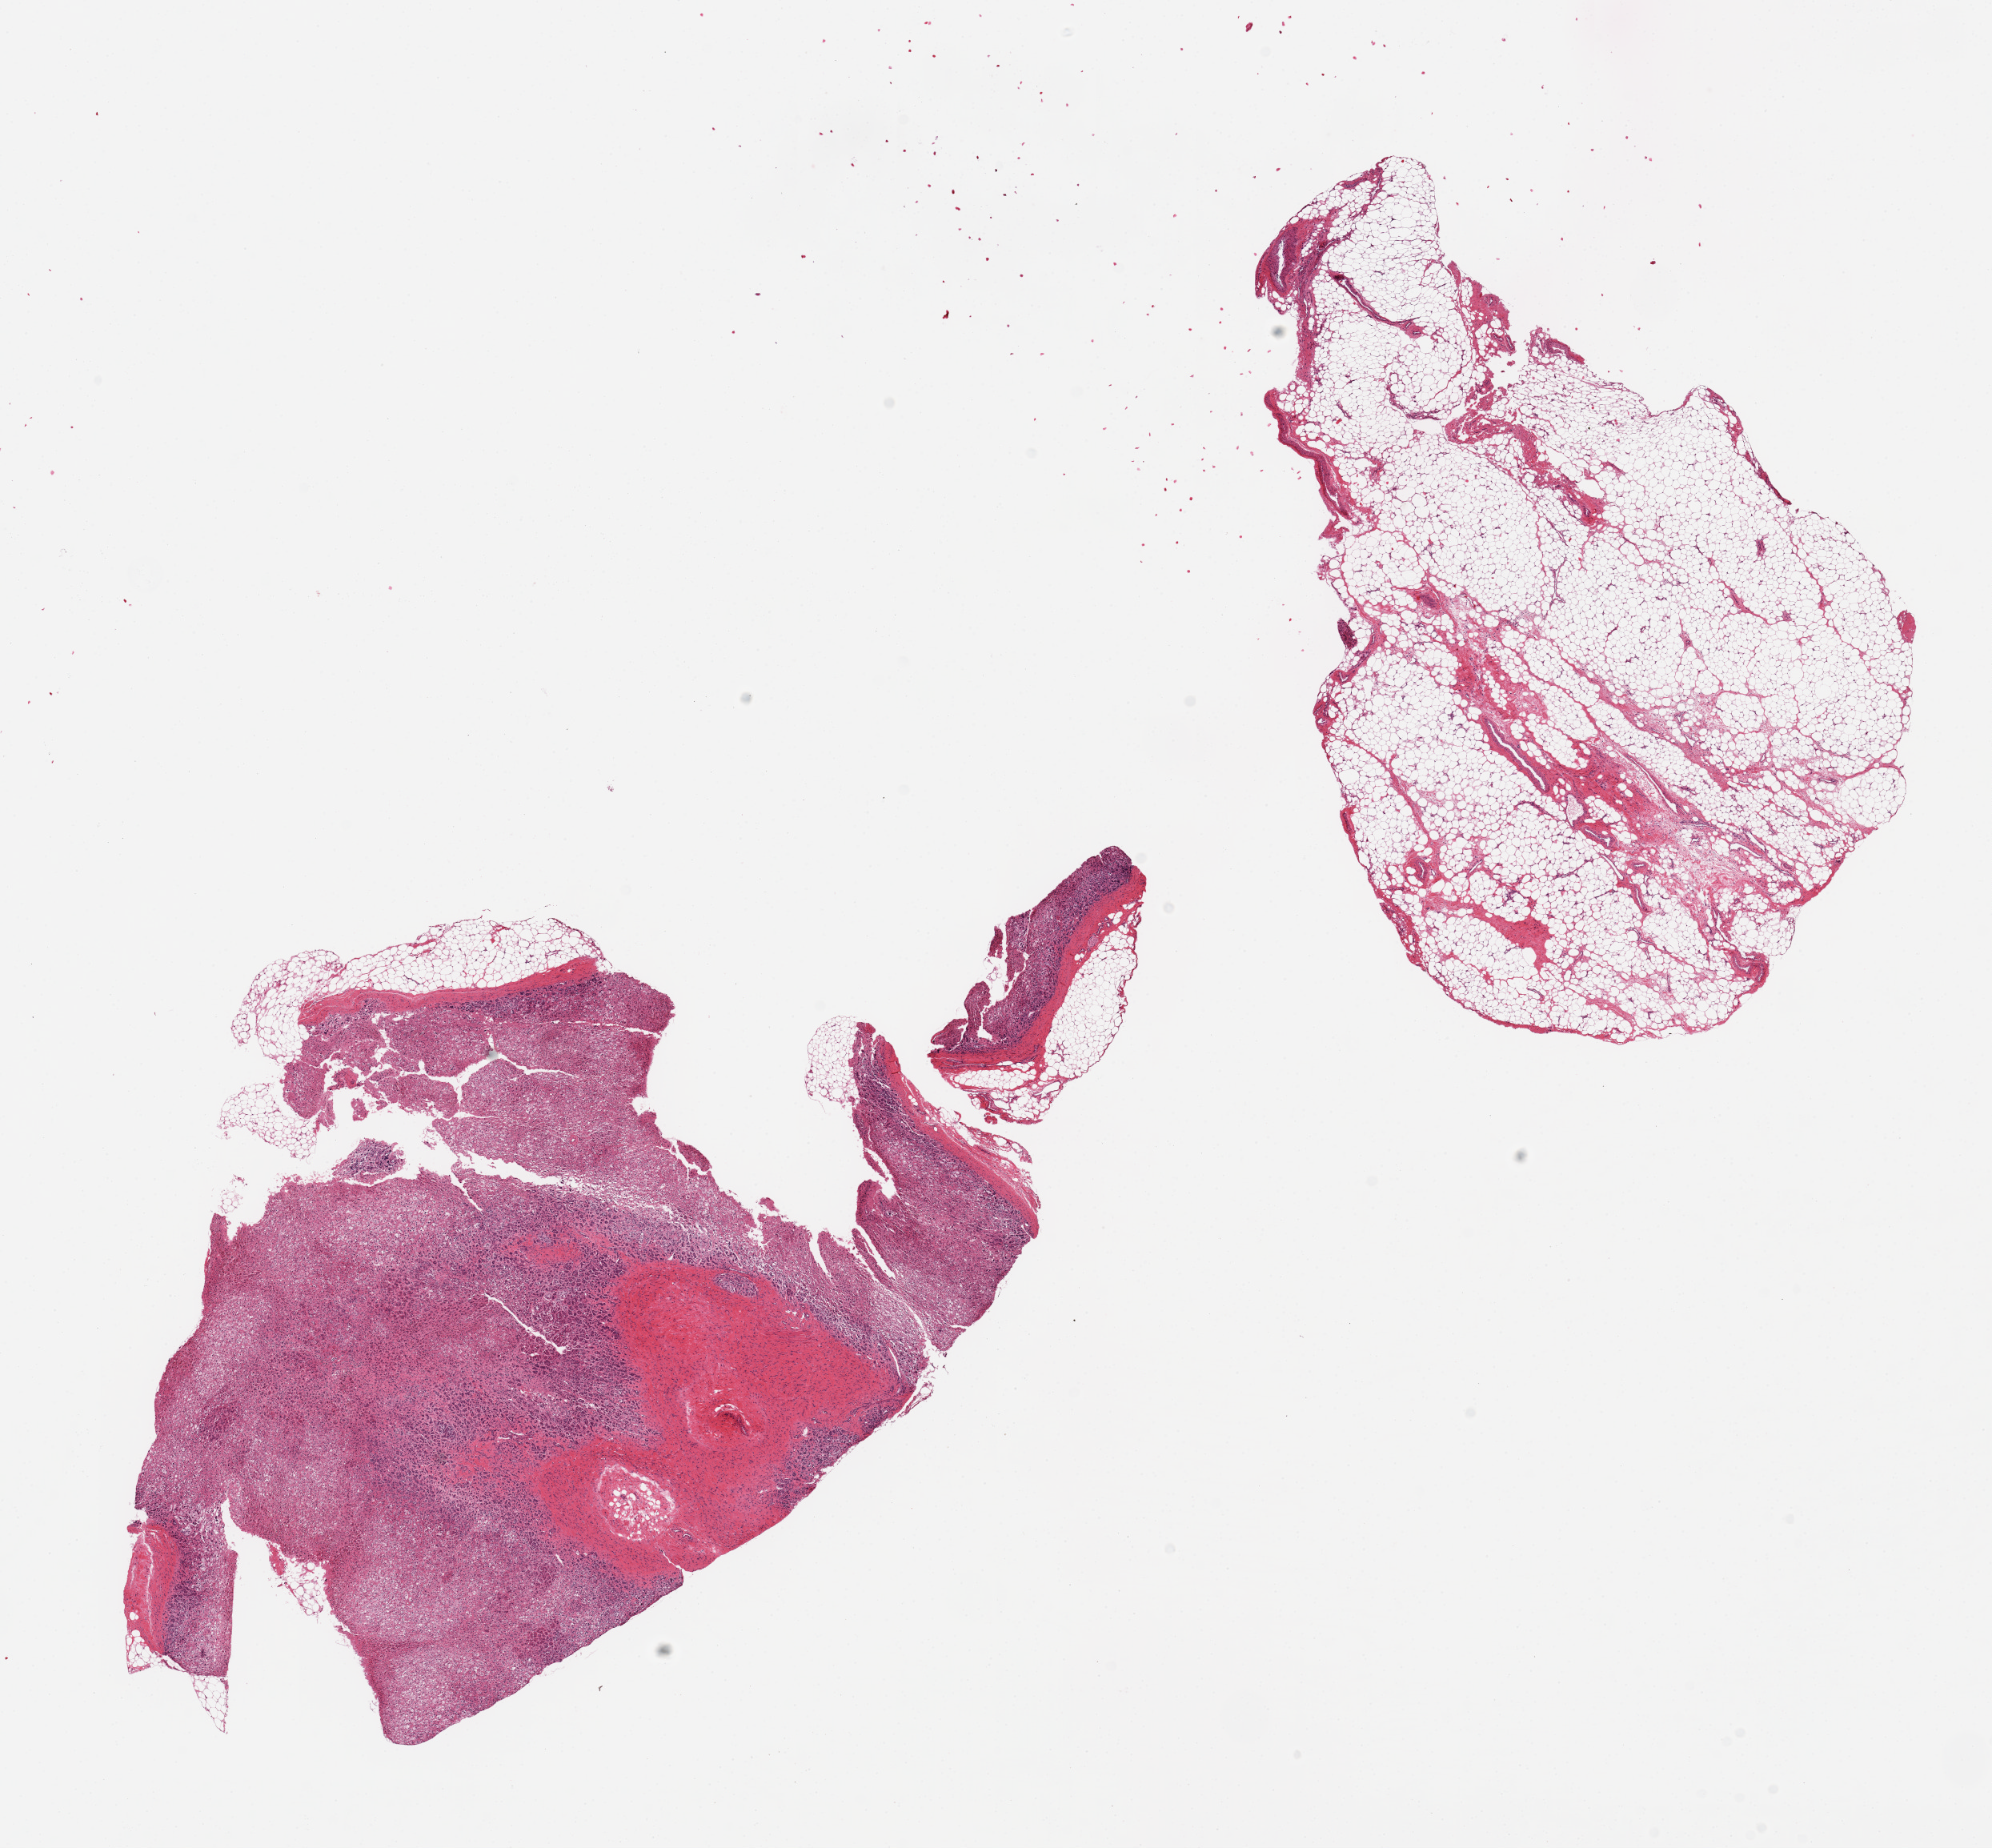
Hematoxylin and eosin (H&E) whole-slide image, whole scanned area (about 19.7 x 18.3 mm) shown as a low-resolution overview. PAXgene-fixed, paraffin-embedded tissue. Target tissue: adrenal gland. Tissue donor sample.
Review note (as recorded): 2 pieces; one piece 100% fibrovascular and adipose tissue; second piece 10% external fat and 20% focal fibrosis.